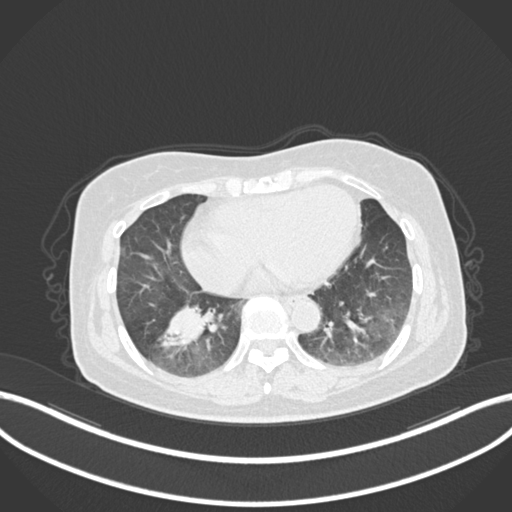
Chest CT, one axial slice; reconstruction kernel B30f; 120 kVp; lung window (W 1500 / L -600 HU); 1 mm slice thickness; 512 × 512 image matrix, field of view 400 × 400 mm. Female patient, age 67 years. Case-level facts recorded for this patient, not image findings: clinical TNM (as recorded): T1c N1 M0.
Structures marked on this image (bounding box drawn by a radiologist):
- lung tumour (recorded histology: adenocarcinoma): bounding box <157,297,212,353> (left, top, right, bottom; pixels)